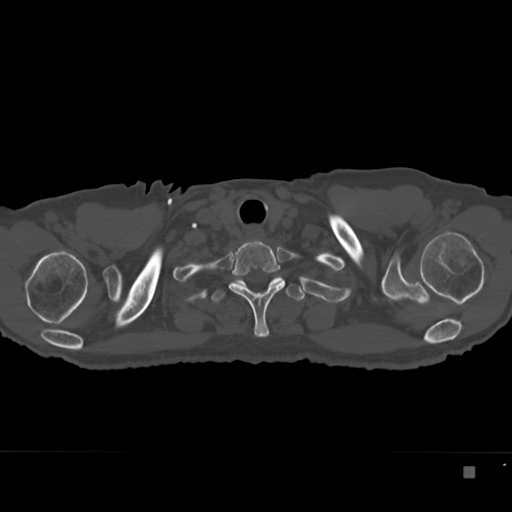
CT including the spine, one axial slice; reconstruction kernel Br40s; 120 kVp; bone window (W 1800 / L 400 HU); 1.5 mm slice thickness; 512 × 512 image matrix, field of view 389 × 389 mm. Patient: male, 72 years. Case-level facts recorded for this patient, not image findings: primary cancer: skeletal.
Outlined on this slice (semi-automatically segmented with operator editing):
- T1 vertebra: box from (x=229, y=240) to (x=285, y=337) px
- T2 vertebra: (x=211, y=274)–(x=306, y=303)